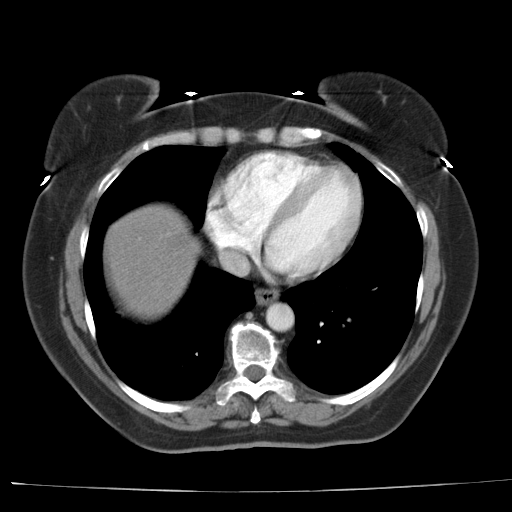
Contrast-enhanced abdominal CT, one axial slice; position 36 of 44 along the scan axis; reconstruction kernel AA-1; 140 kVp; intravenous contrast given; soft-tissue window (W 400 / L 40 HU); 512 × 512 image matrix, field of view 373 × 373 mm. Female patient. Case-level facts recorded for this patient, not image findings: diagnosis: colorectal cancer liver metastases, imaged before liver resection; multiple liver metastases: yes; largest metastasis: 1.8 cm; chemotherapy before resection: yes.
Outlined on this slice (manually delineated by an expert):
- liver: box from (x=104, y=204) to (x=201, y=322) px
- planned liver remnant (the part of the liver to remain after resection): (x=148, y=203)–(x=196, y=240)